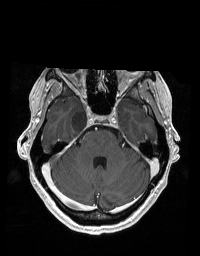
Brain MRI from a brain-tumour surgery series, one axial slice; position 130 of 192 along the scan axis; T1-weighted post-contrast; 200 × 256 image matrix, field of view 195 × 250 mm. From the clinical record (not read from this slice): histopathology: Glioblastoma; WHO grade: 2; IDH mutation: no; tumour location: Right Skull Base Temporal.
Structures marked on this image (manually delineated by an expert):
- tumour: bounding box (x1, y1, x2, y2) in pixels: (72, 109, 87, 132)